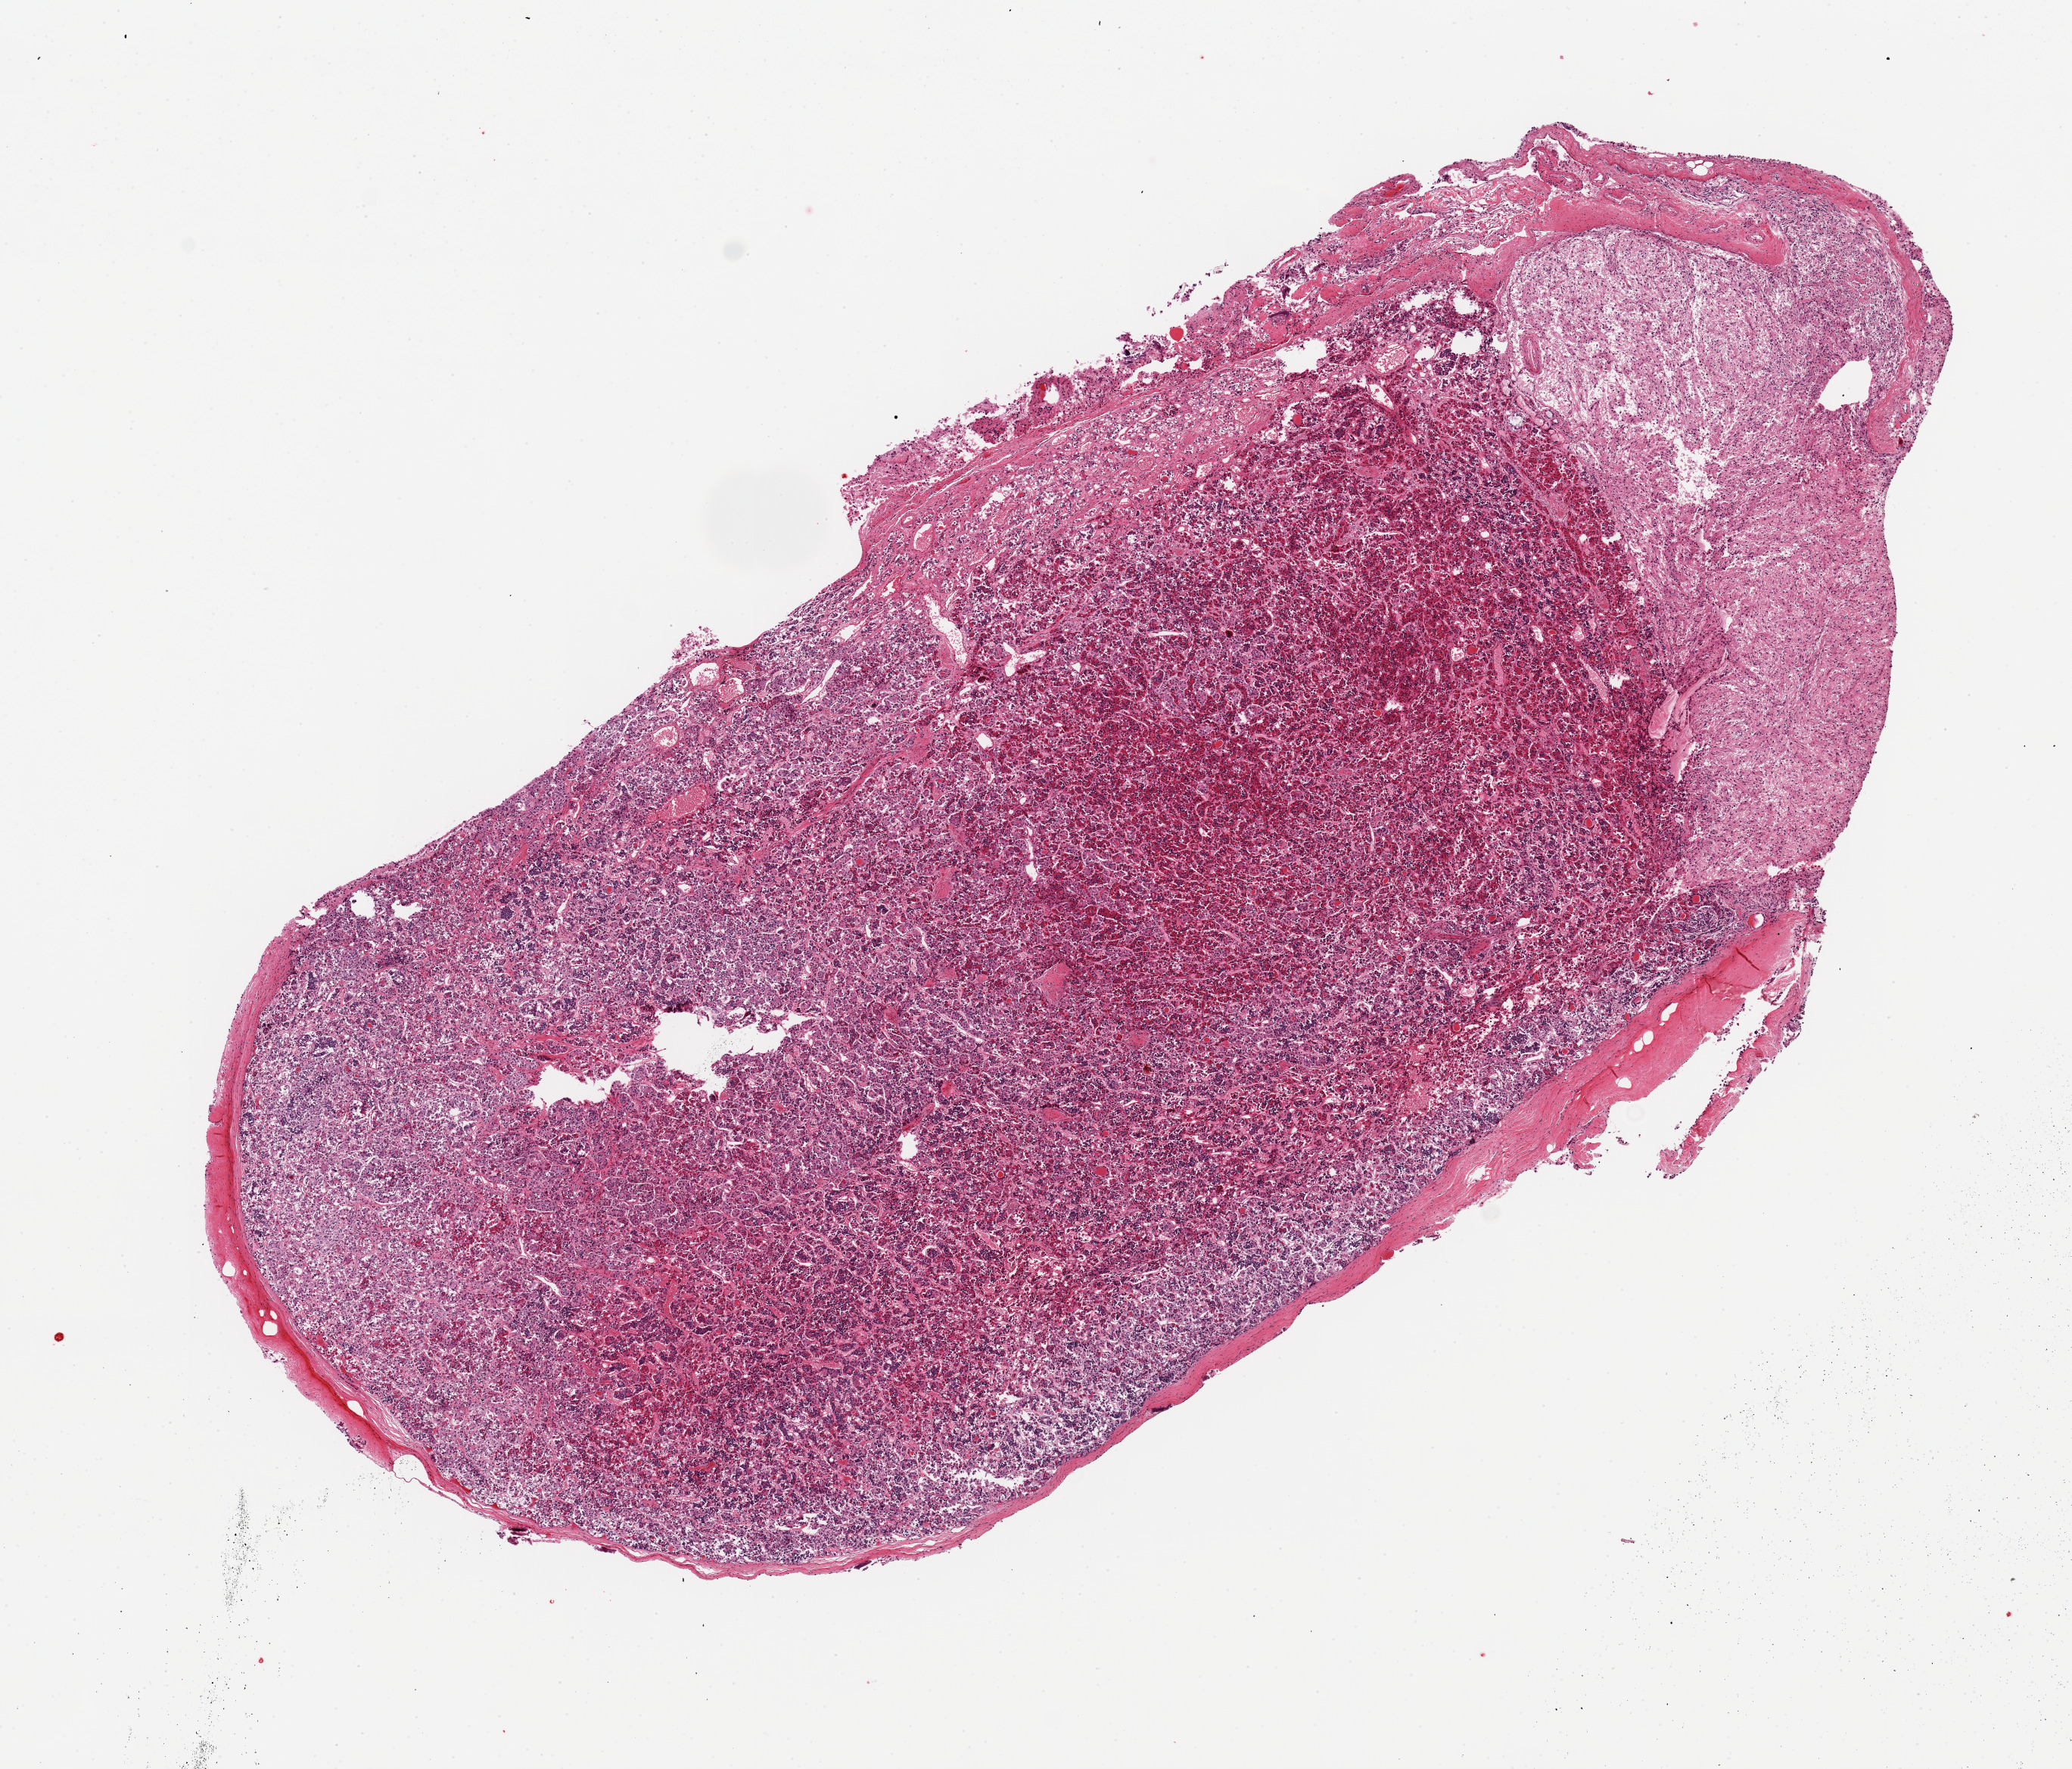
Haematoxylin and eosin whole-slide image — shown as a low-resolution overview of the whole scanned area (about 10.8 x 9.2 mm), PAXgene-fixed, paraffin-embedded tissue, section of pituitary (target tissue), tissue donor sample. Donor: female.
Review note (as recorded): 10x5mm aliquot with 3.5x2mm portion of neuohypophysis appended.